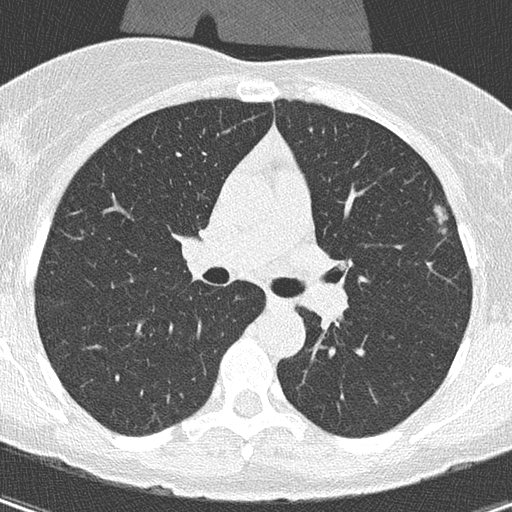
Chest CT (low-dose screening protocol), one axial image; first (baseline) screen; lung window (W 1500 / L -600 HU); lung (sharp) reconstruction kernel (B50f); slice 114 of 305 in the series. Female participant, aged 56 years at enrolment. Former smoker at enrolment.
Expert reader's lesion annotation, box from (x=420, y=194) to (x=465, y=250) px. The exam's reader record, not a measurement of the box and not confirmed to be the same lesion: non-calcified nodule or mass ≥4 mm, left upper lobe, 110 × 106 mm, spiculated (stellate) margins, soft tissue attenuation. Official screen result: positive, change unspecified: nodule(s) >= 4 mm or enlarging nodule(s), mass(es), or other non-specific abnormalities suspicious for lung cancer. Later outcome: lung cancer diagnosed 417 days after this screen (after the second annual screen) — adenocarcinoma, NOS, left upper lobe, moderately differentiated (G2), stage IA (AJCC 6th edition), 11 mm at pathology.